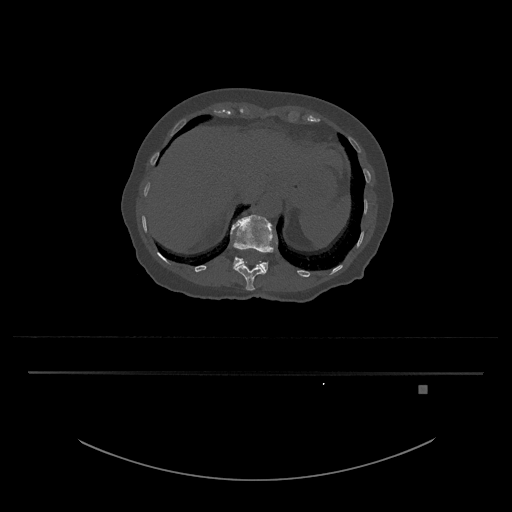
CT including the spine, one axial slice; position 586 of 797 along the scan axis; bone window (W 1800 / L 400 HU); 0.5 mm slice thickness; 512 × 512 image matrix, field of view 500 × 500 mm. Female patient, age 57 years. From the clinical record (not read from this slice): primary cancer: cervical.
Outlined on this slice (semi-automatically segmented with operator editing):
- L1 vertebra: bounding box [x1, y1, x2, y2] px = [231, 215, 278, 272]
- T12 vertebra: [235, 262, 266, 291]